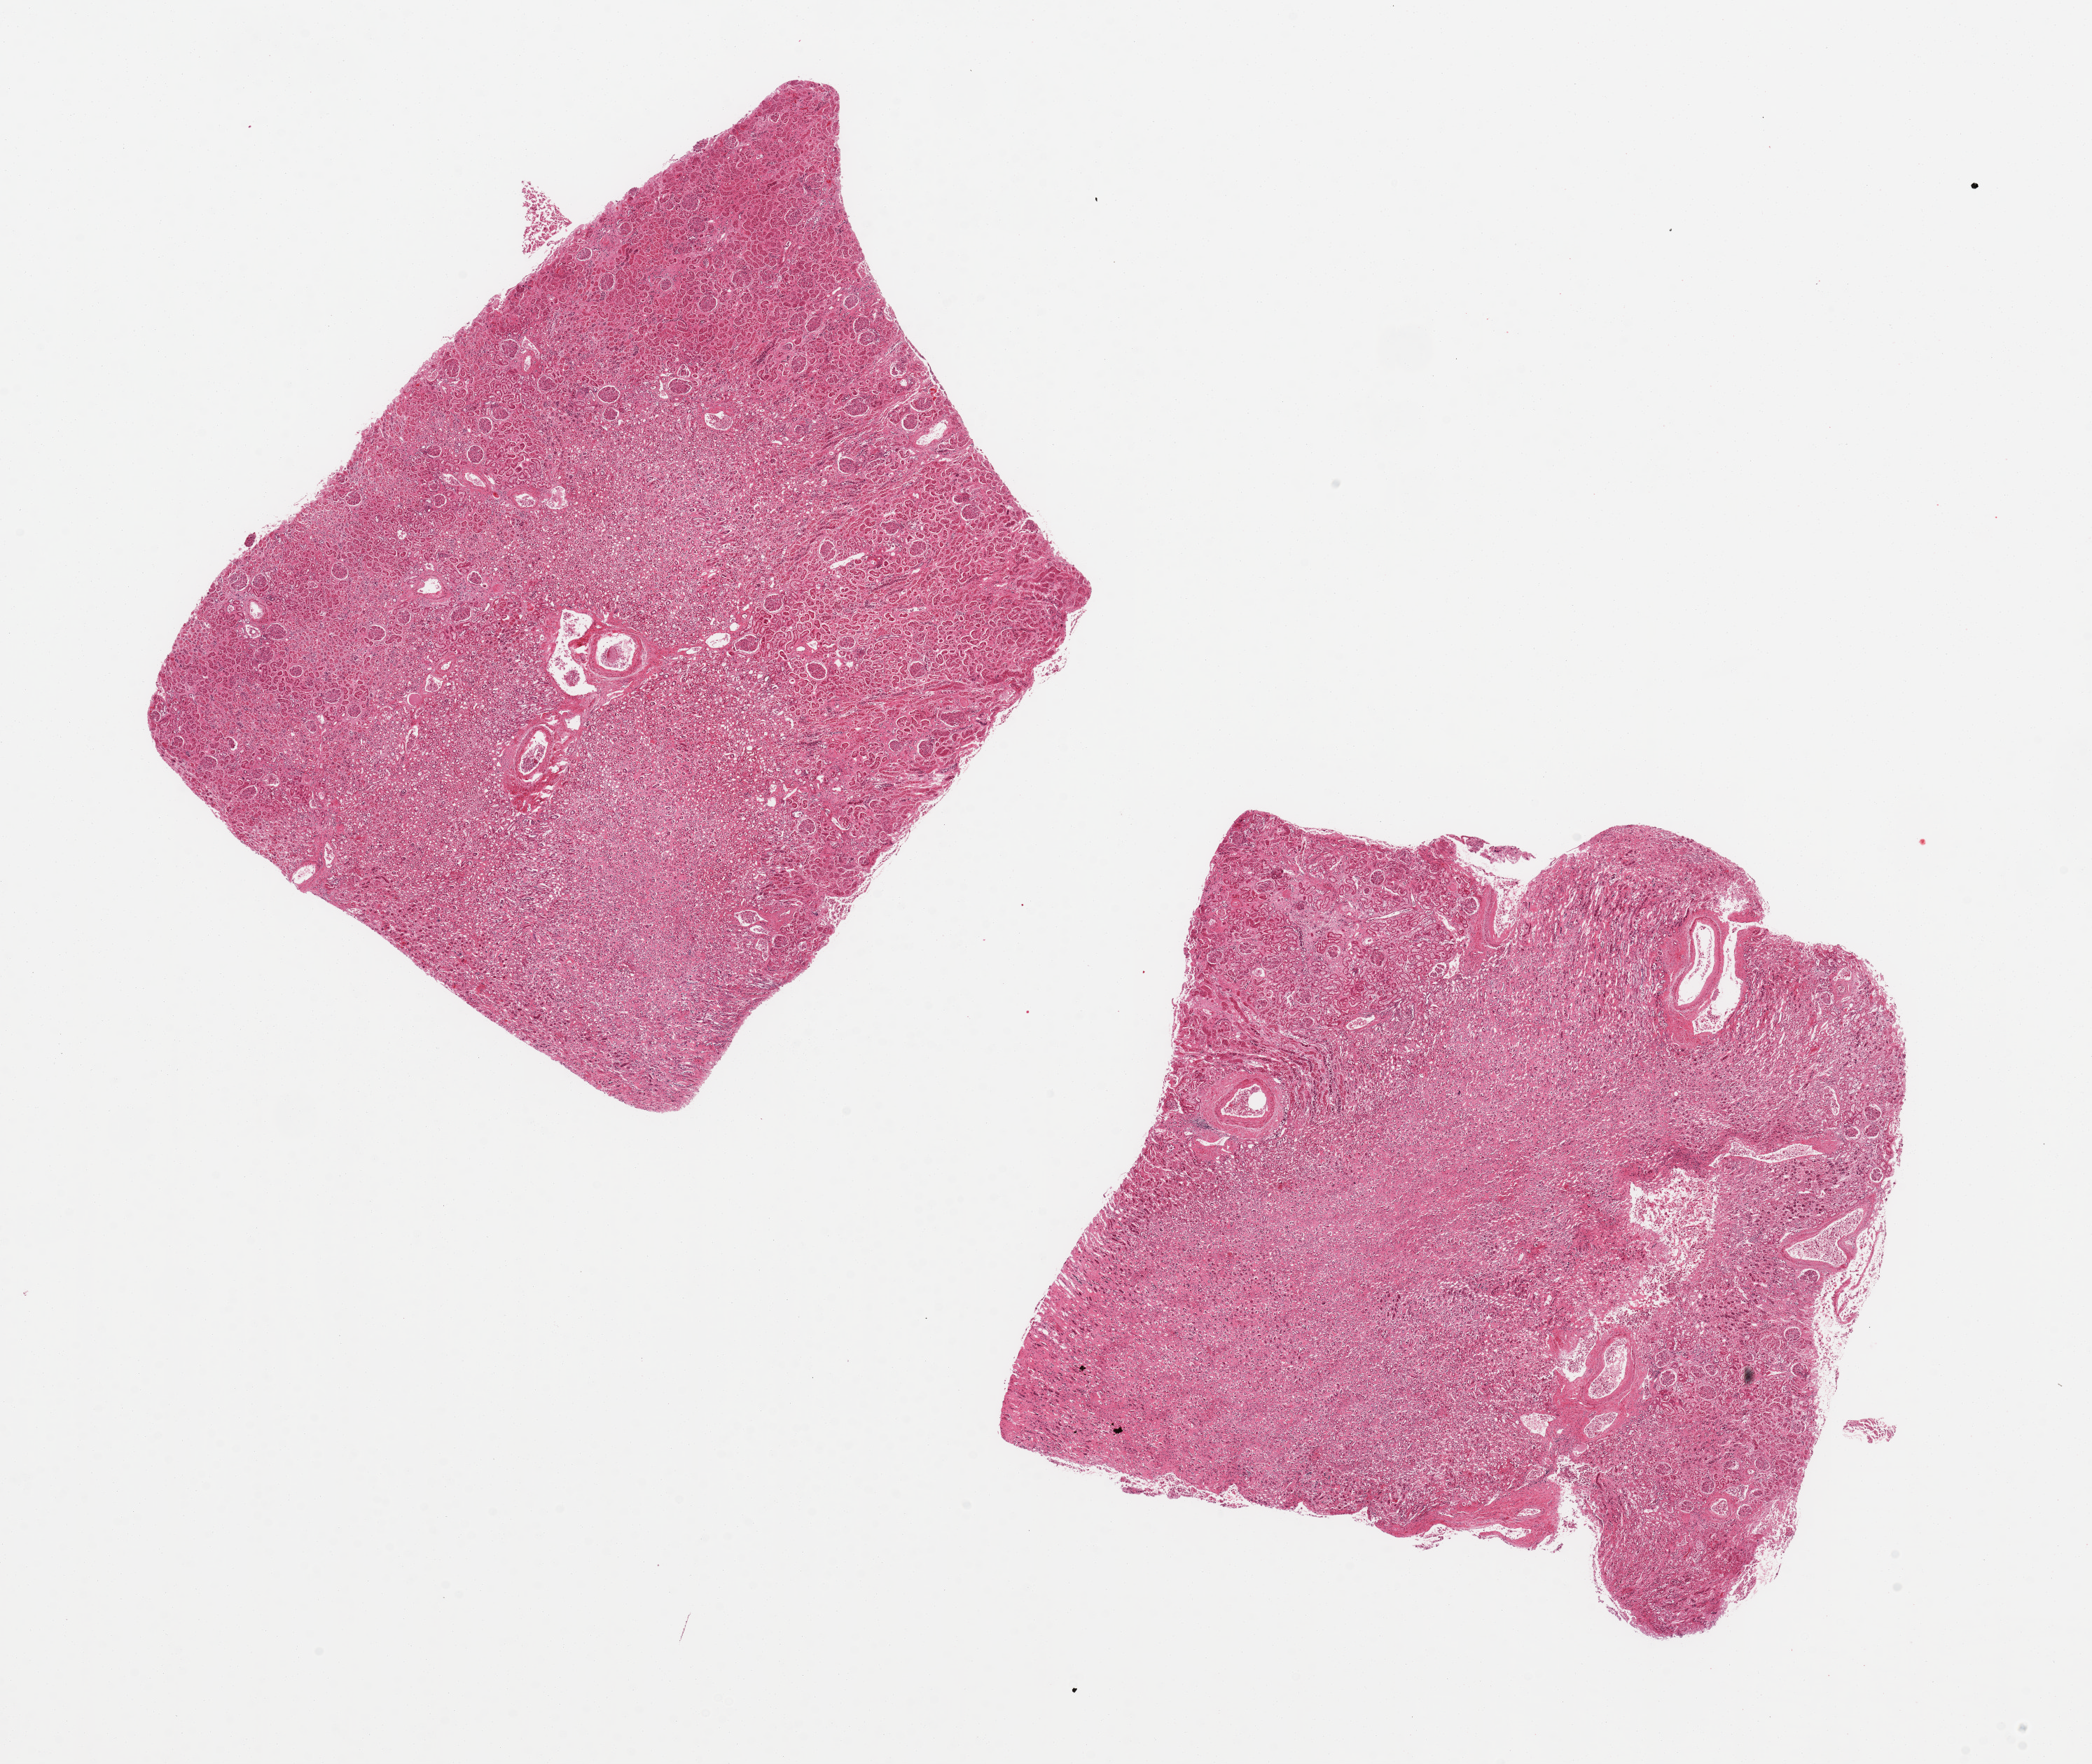
Digitized H&E-stained section — shown as a low-resolution overview of the whole scanned area (about 23.6 x 19.9 mm, acquisition: 20x scan); PAXgene-fixed paraffin-embedded (PFPE) section; target tissue: renal medulla; tissue donor sample. Donor sex: male.
Review note (as recorded): 2 pieces, 8x8 & 9x7 mm; each have mixture of cortex and medulla in about equal parts.